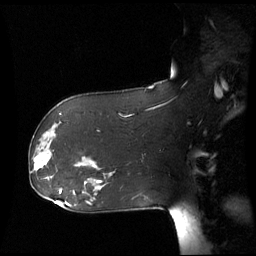
Breast MRI (dynamic contrast-enhanced), one sagittal slice; slice 38 of 60 in the series (ordered by position); dynamic contrast-enhanced series, image 2 of 3 at this slice position (ordered by acquisition); 1.5 T; TE 4.2 ms, TR 8.9 ms; 2.7 mm slice thickness; 256 × 256 image matrix, field of view 280 × 280 mm. Female patient, age 61 years. From the clinical record (not read from this slice): setting: breast cancer imaged before/during neoadjuvant chemotherapy; receptor status: HR-positive, HER2-negative.
Outlined on this slice (semi-automatically segmented with operator editing):
- analysis volume of interest (the breast-tissue region the enhancement analysis was run in; not a lesion): bounding box <30,142,55,177> (left, top, right, bottom; pixels)
- tumour enhancement mask (voxels above the 70 % enhancement threshold inside the analysis volume of interest): <34,154,49,169>